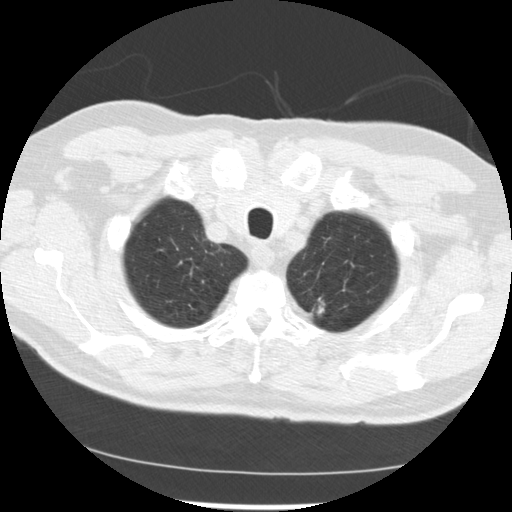
Low-dose screening chest CT, one axial slice. Slice 220 of 249 in the series (ordered by position). Reconstruction kernel STANDARD. 120 kVp. Lung window (W 1500 / L -600 HU). 512 × 512 image matrix.
Annotated regions visible in this slice (outlined manually by an expert reader):
- lesion 2 (tumor, upper lobe of left lung): bounding box (x1, y1, x2, y2) in pixels: (318, 300, 324, 314)